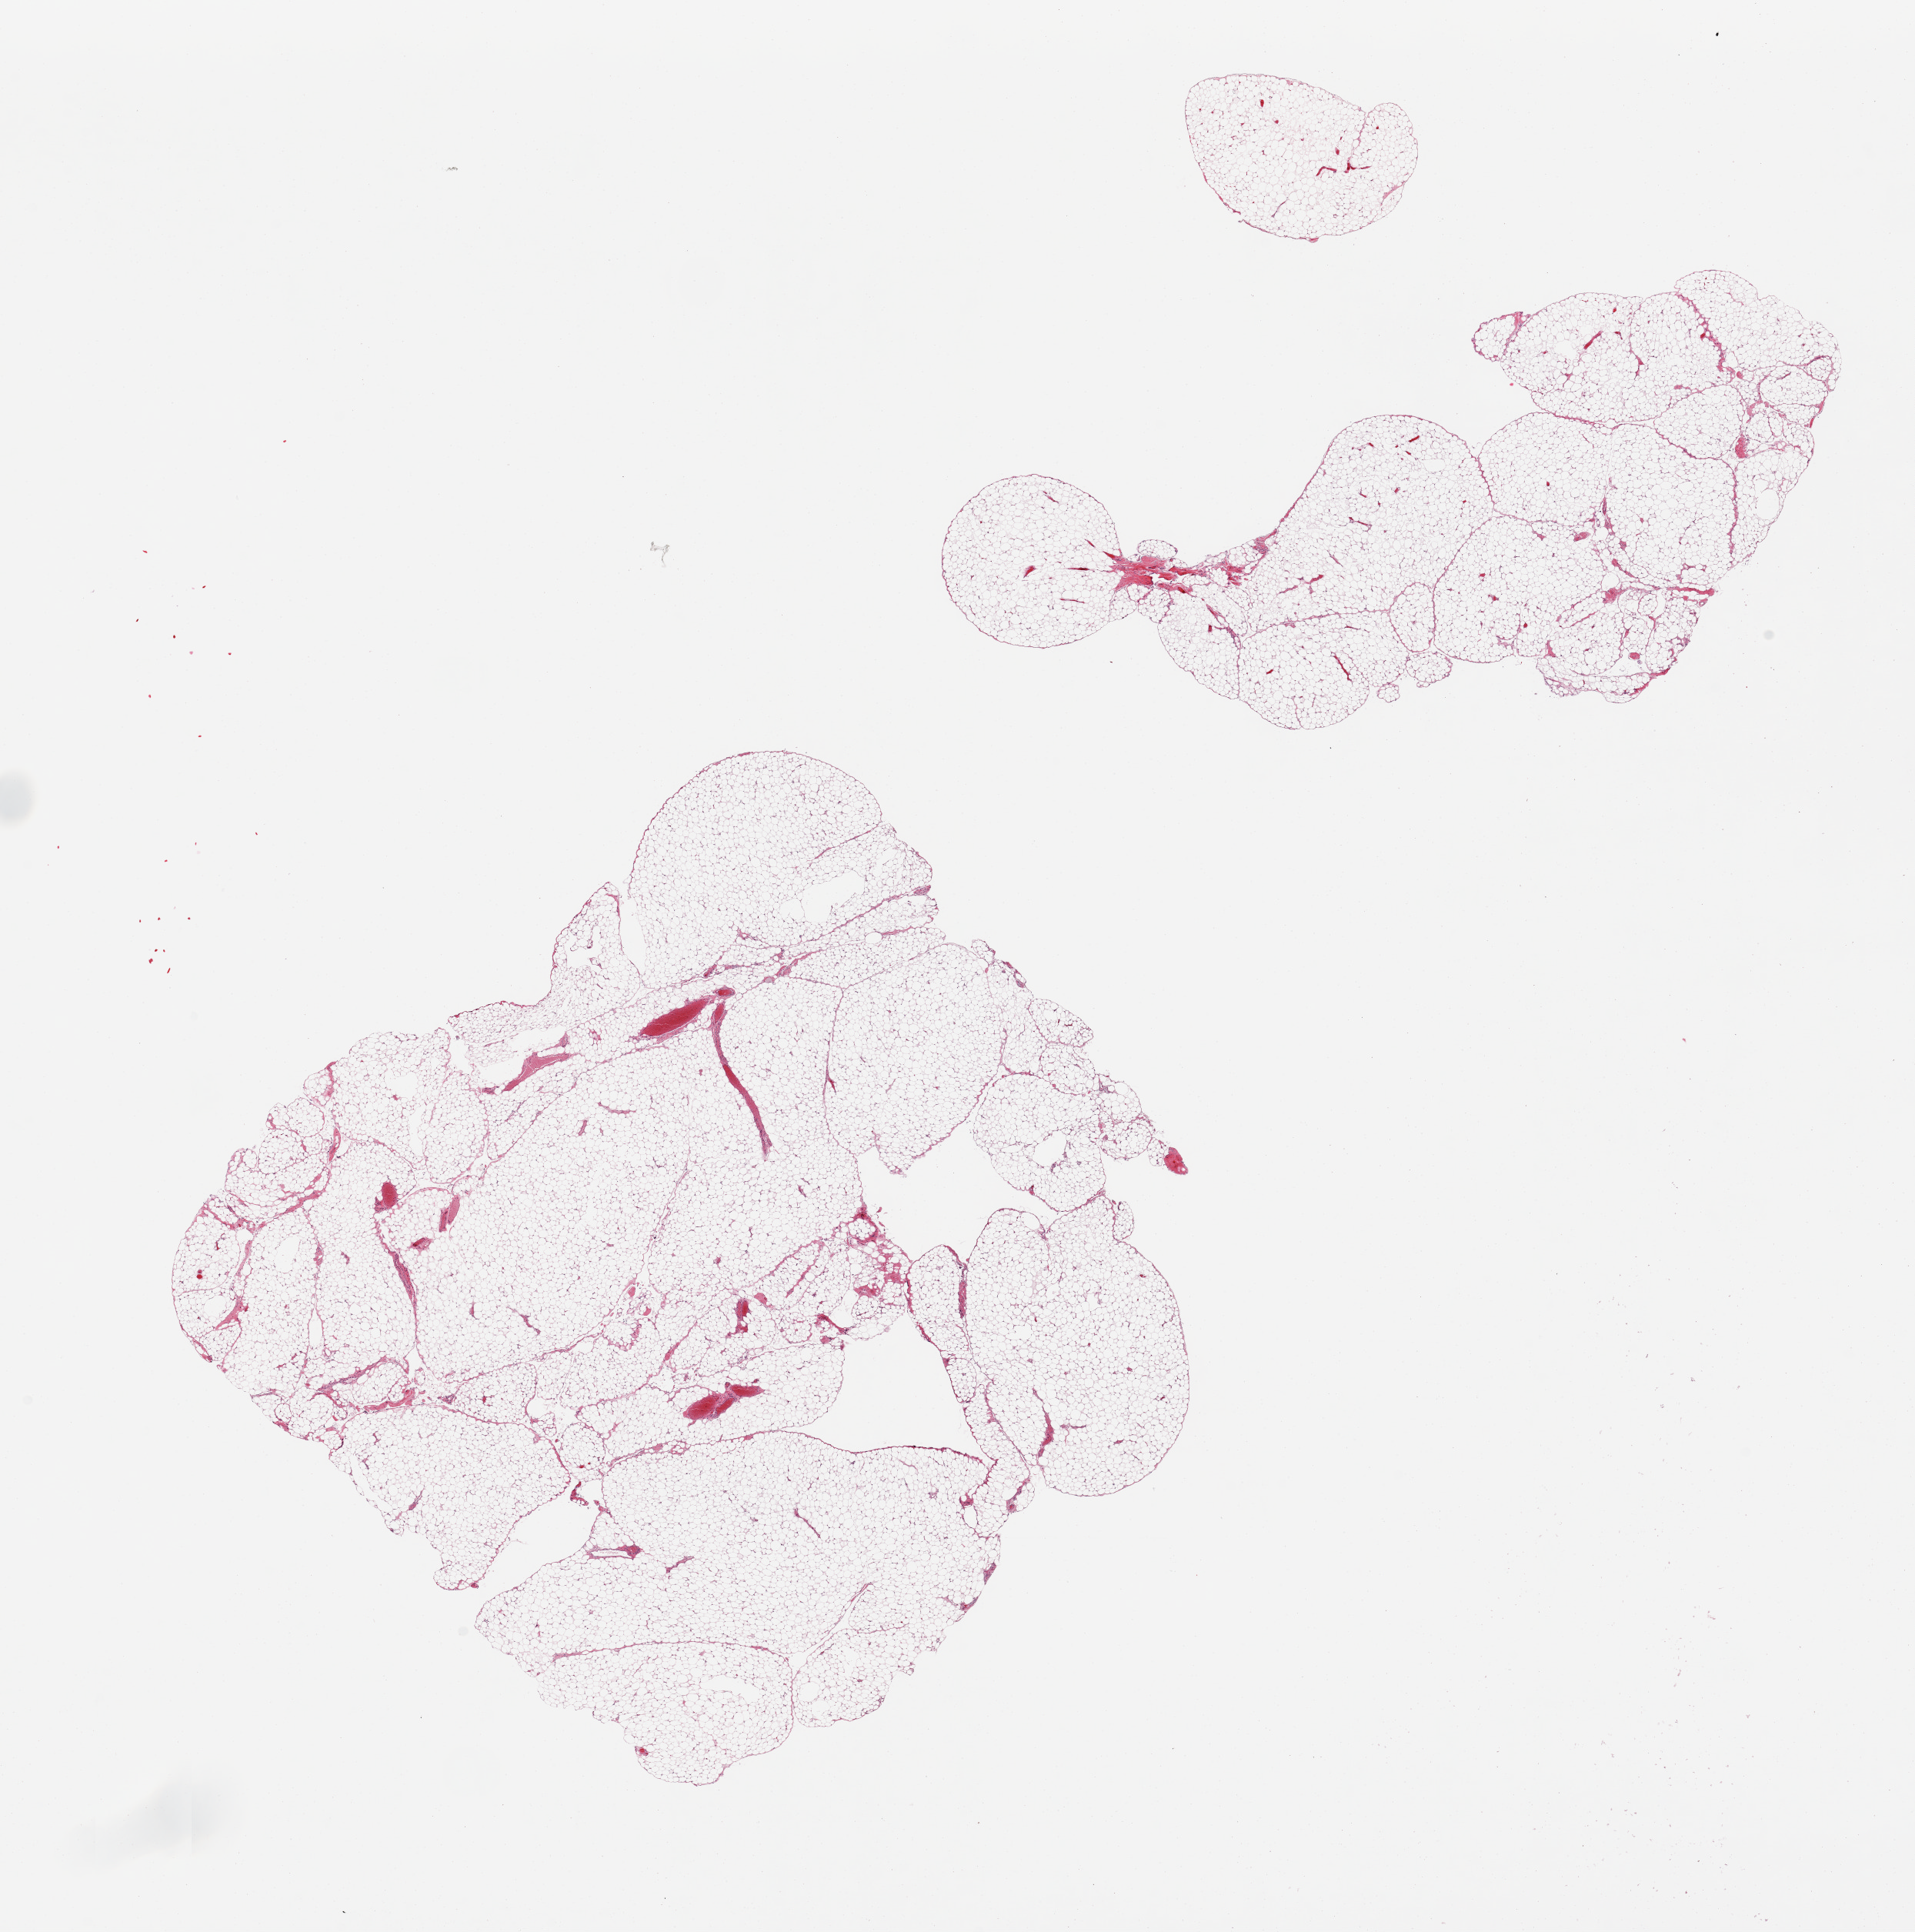
Haematoxylin and eosin whole-slide image, a low-resolution overview of the entire scanned area, about 19.7 x 19.9 mm (from a 20x scan), PAXgene-fixed, paraffin-embedded tissue, sampled site (target tissue): omentum, donor tissue sample. Donor sex: male.
Pathologist's review note for this sample: 2 pieces.